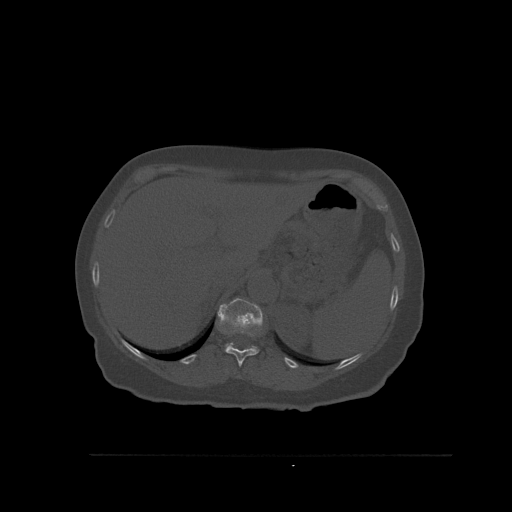
CT including the spine, one axial slice. Slice 298 of 527 in the series (ordered by position). Bone window (W 1800 / L 400 HU). 1.5 mm slice thickness. 512 × 512 image matrix, field of view 470 × 470 mm. Patient: female, 73 years. Case-level facts recorded for this patient, not image findings: primary cancer: breast; vertebrae with lytic lesions (as recorded): L2.
Structures marked on this image (semi-automatic segmentation, software-assisted and operator-edited):
- T11 vertebra: bounding box [x1, y1, x2, y2] px = [225, 332, 259, 367]
- T12 vertebra: [217, 298, 263, 350]